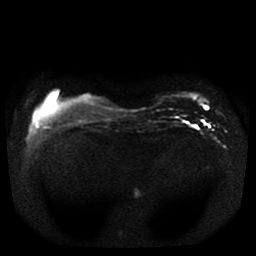
Breast MRI, one axial slice. Position 6 of 41 along the scan axis. Diffusion-weighted series; image 2 of 4 stored at this slice position (different b-values; order by instance number). 1.5 T. 256 × 256 image matrix, field of view 330 × 330 mm. Female patient.
Outlined on this slice (expert manual segmentation):
- tumour on diffusion-weighted imaging: bounding box (x1, y1, x2, y2) in pixels: (203, 105, 208, 109)